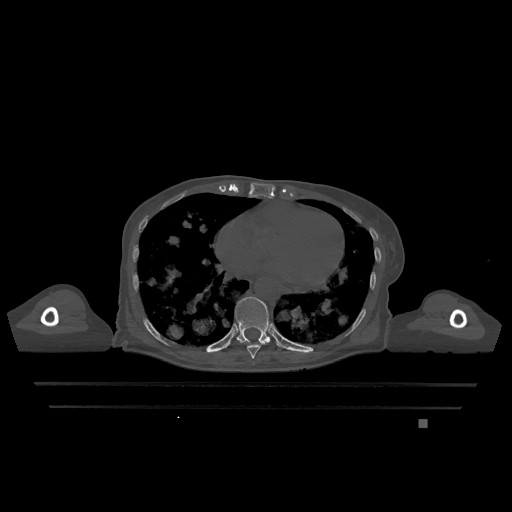
CT including the spine, one axial slice; slice 666 of 1317 in the series (ordered by position); bone window (W 1800 / L 400 HU); 512 × 512 image matrix. Patient: female, 74 years. Case-level facts recorded for this patient, not image findings: primary cancer: lung.
Structures marked on this image (semi-automatic segmentation, software-assisted and operator-edited):
- T10 vertebra: bounding box (x1, y1, x2, y2) in pixels: (235, 297, 271, 343)
- T9 vertebra: (240, 340, 270, 359)